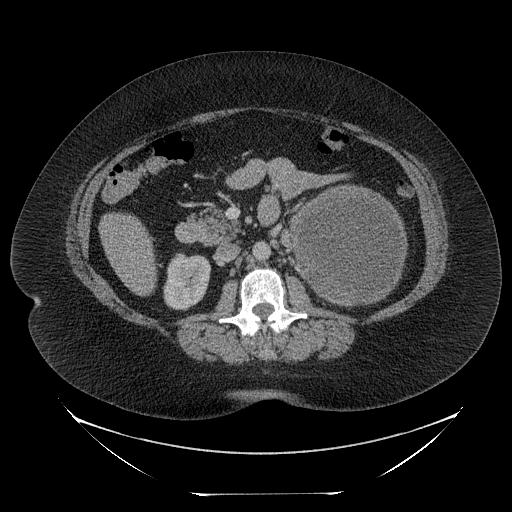
Contrast-enhanced abdominal CT, one axial slice; slice 124 of 205 in the series (ordered by position); reconstruction kernel STANDARD; 120 kVp; intravenous contrast given; soft-tissue window (W 400 / L 40 HU); 2.5 mm slice thickness; 512 × 512 image matrix, field of view 500 × 500 mm. Patient: female, 53 years. Case-level facts recorded for this patient, not image findings: diagnosis: adrenocortical carcinoma; tumour side: left adrenal; tumour size at pathology: 17 cm; Ki-67 index: 20 %; stage (as recorded): 3.
Structures marked on this image (semi-automatically segmented with operator editing):
- mass: bounding box <294,189,405,303> (left, top, right, bottom; pixels)